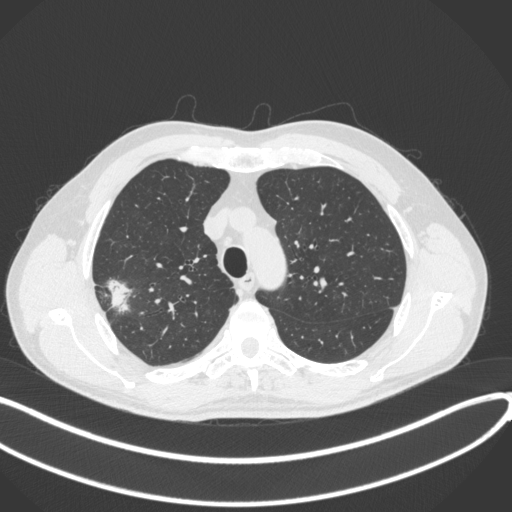
Chest CT, one axial slice; slice 318 of 381 in the series (ordered by position); 120 kVp; lung window (W 1500 / L -600 HU); 512 × 512 image matrix, field of view 400 × 400 mm. Male patient, age 62 years. Case-level facts recorded for this patient, not image findings: clinical TNM (as recorded): T1c N0 M0.
Annotated regions visible in this slice (rectangle marked by the reading radiologist):
- lung tumour (recorded histology: adenocarcinoma): bounding box [x1, y1, x2, y2] px = [102, 275, 130, 316]